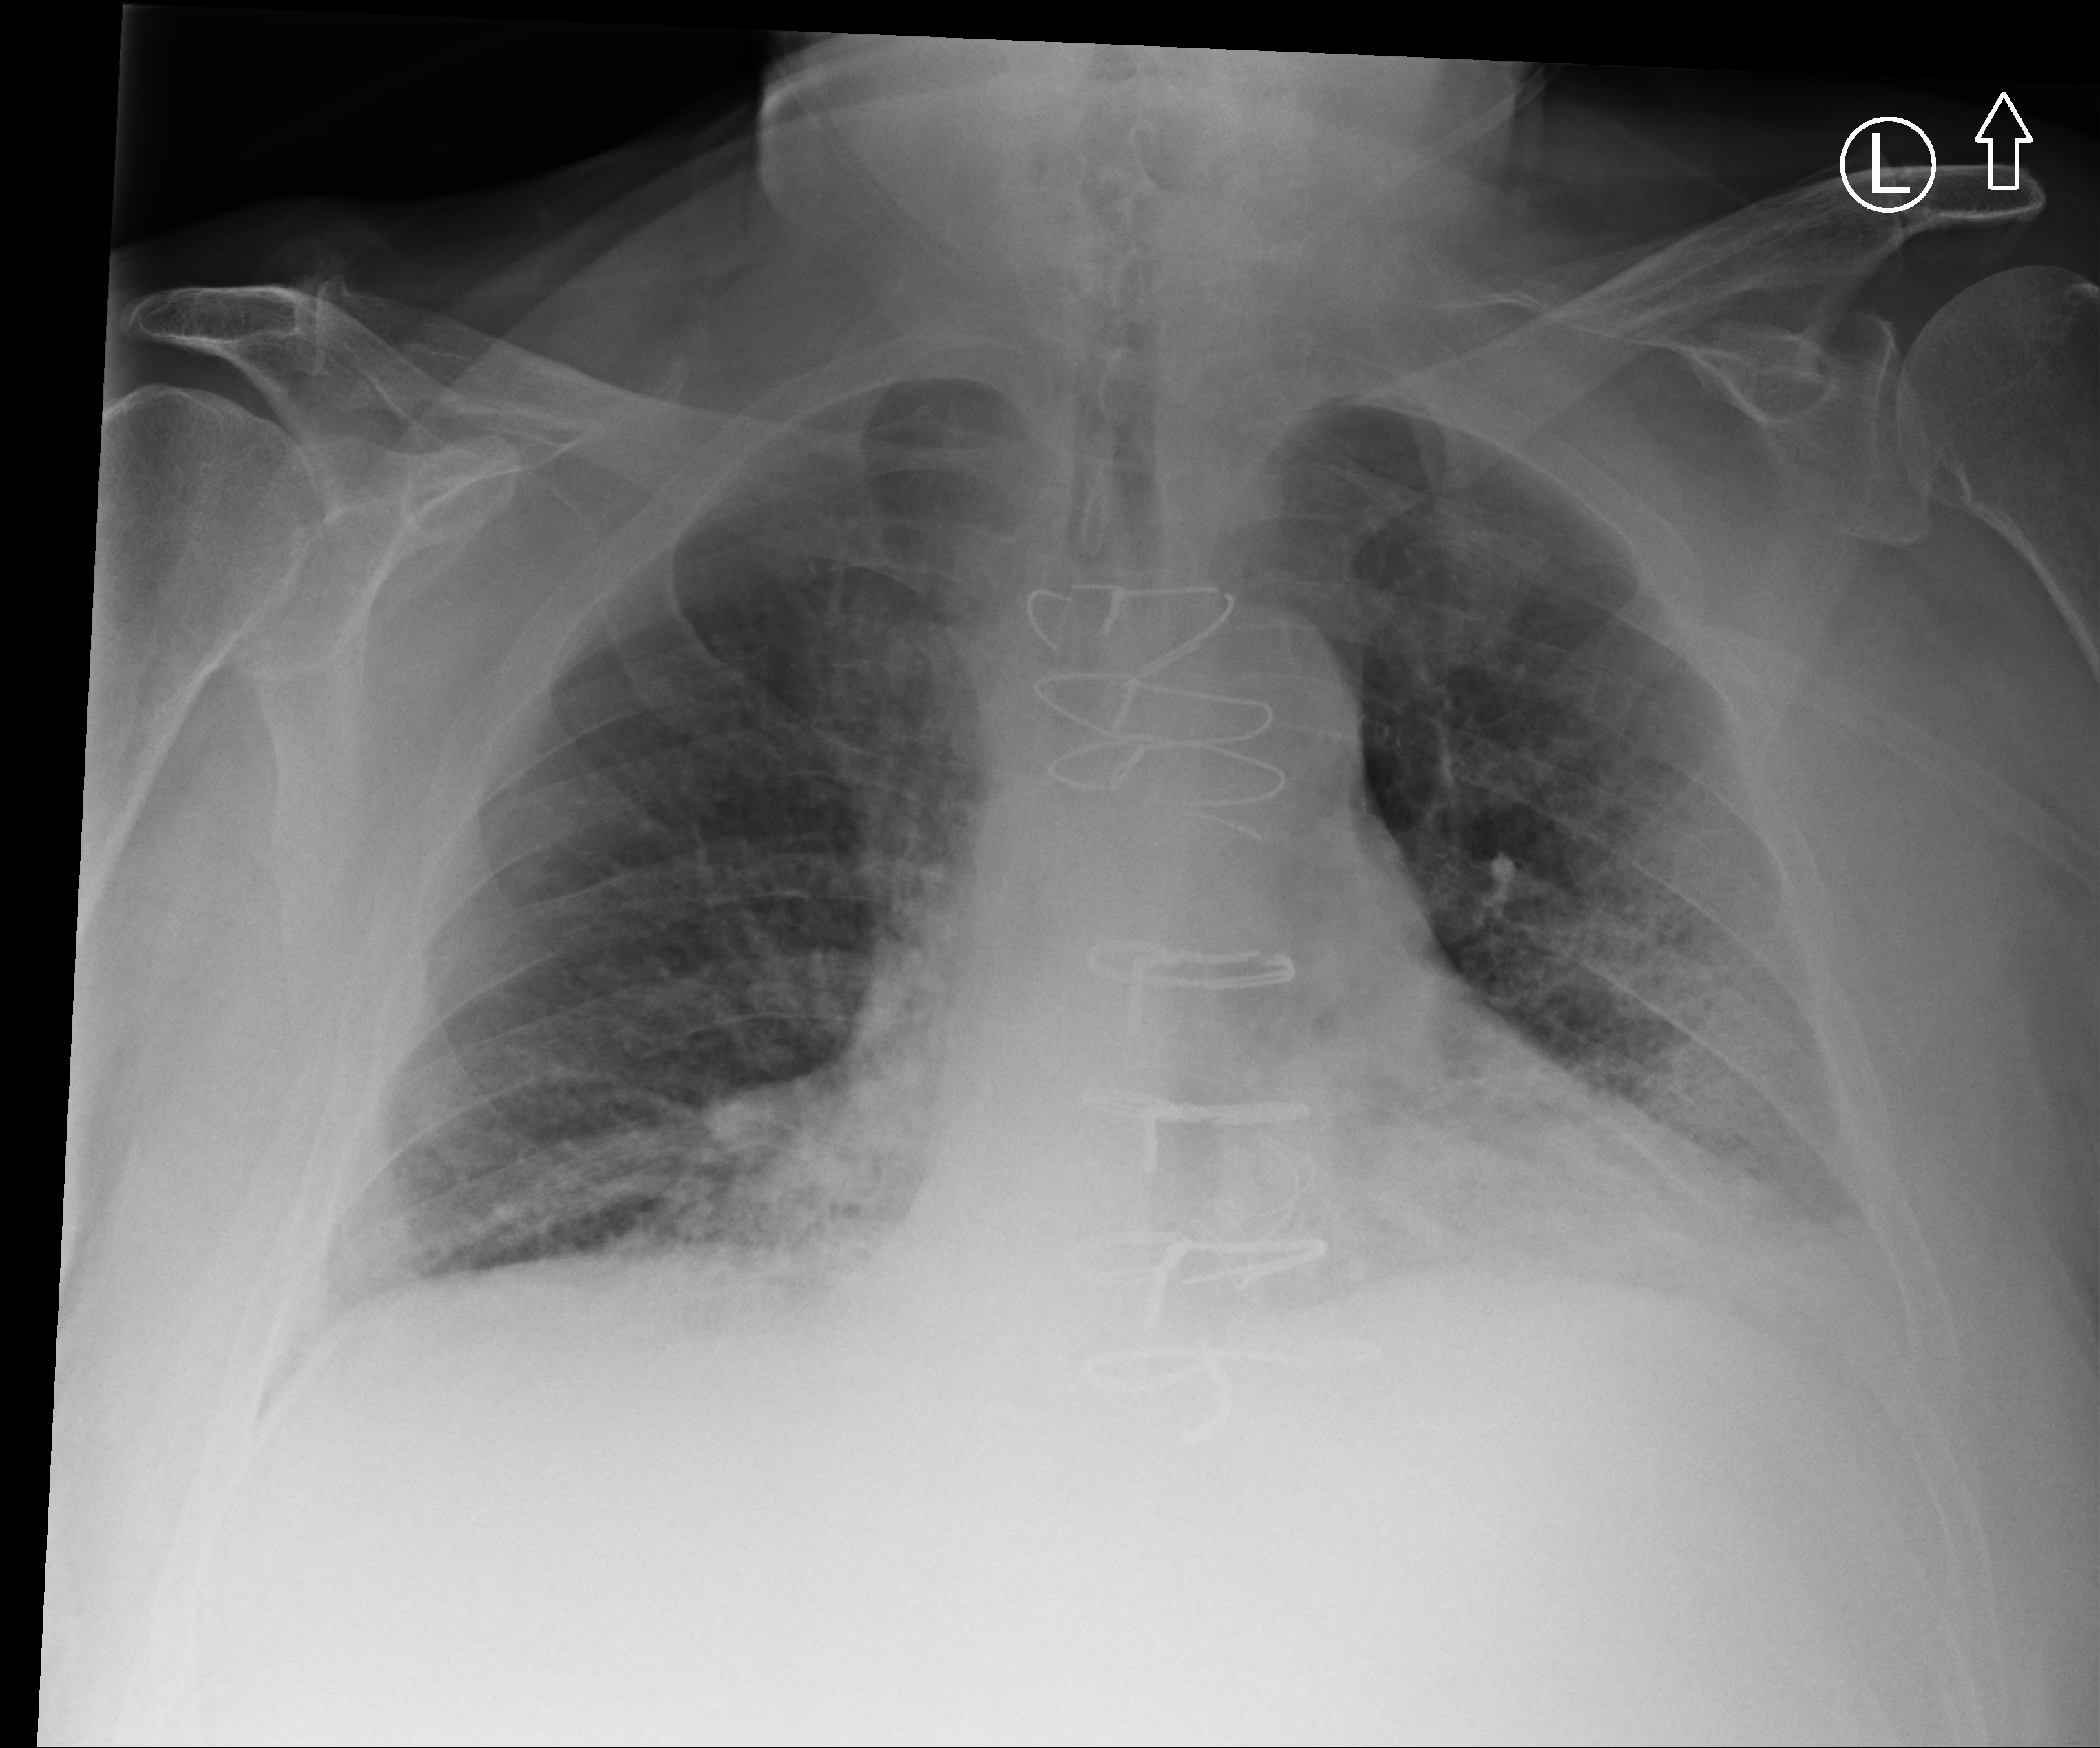
Bedside chest radiograph (computed radiography), anteroposterior (AP) projection. Patient hospitalised with COVID-19; male, aged 75–90 years.
Admission-level facts for this patient (not findings on this image; timing relative to this image not recorded):
- diabetes (admission record): yes